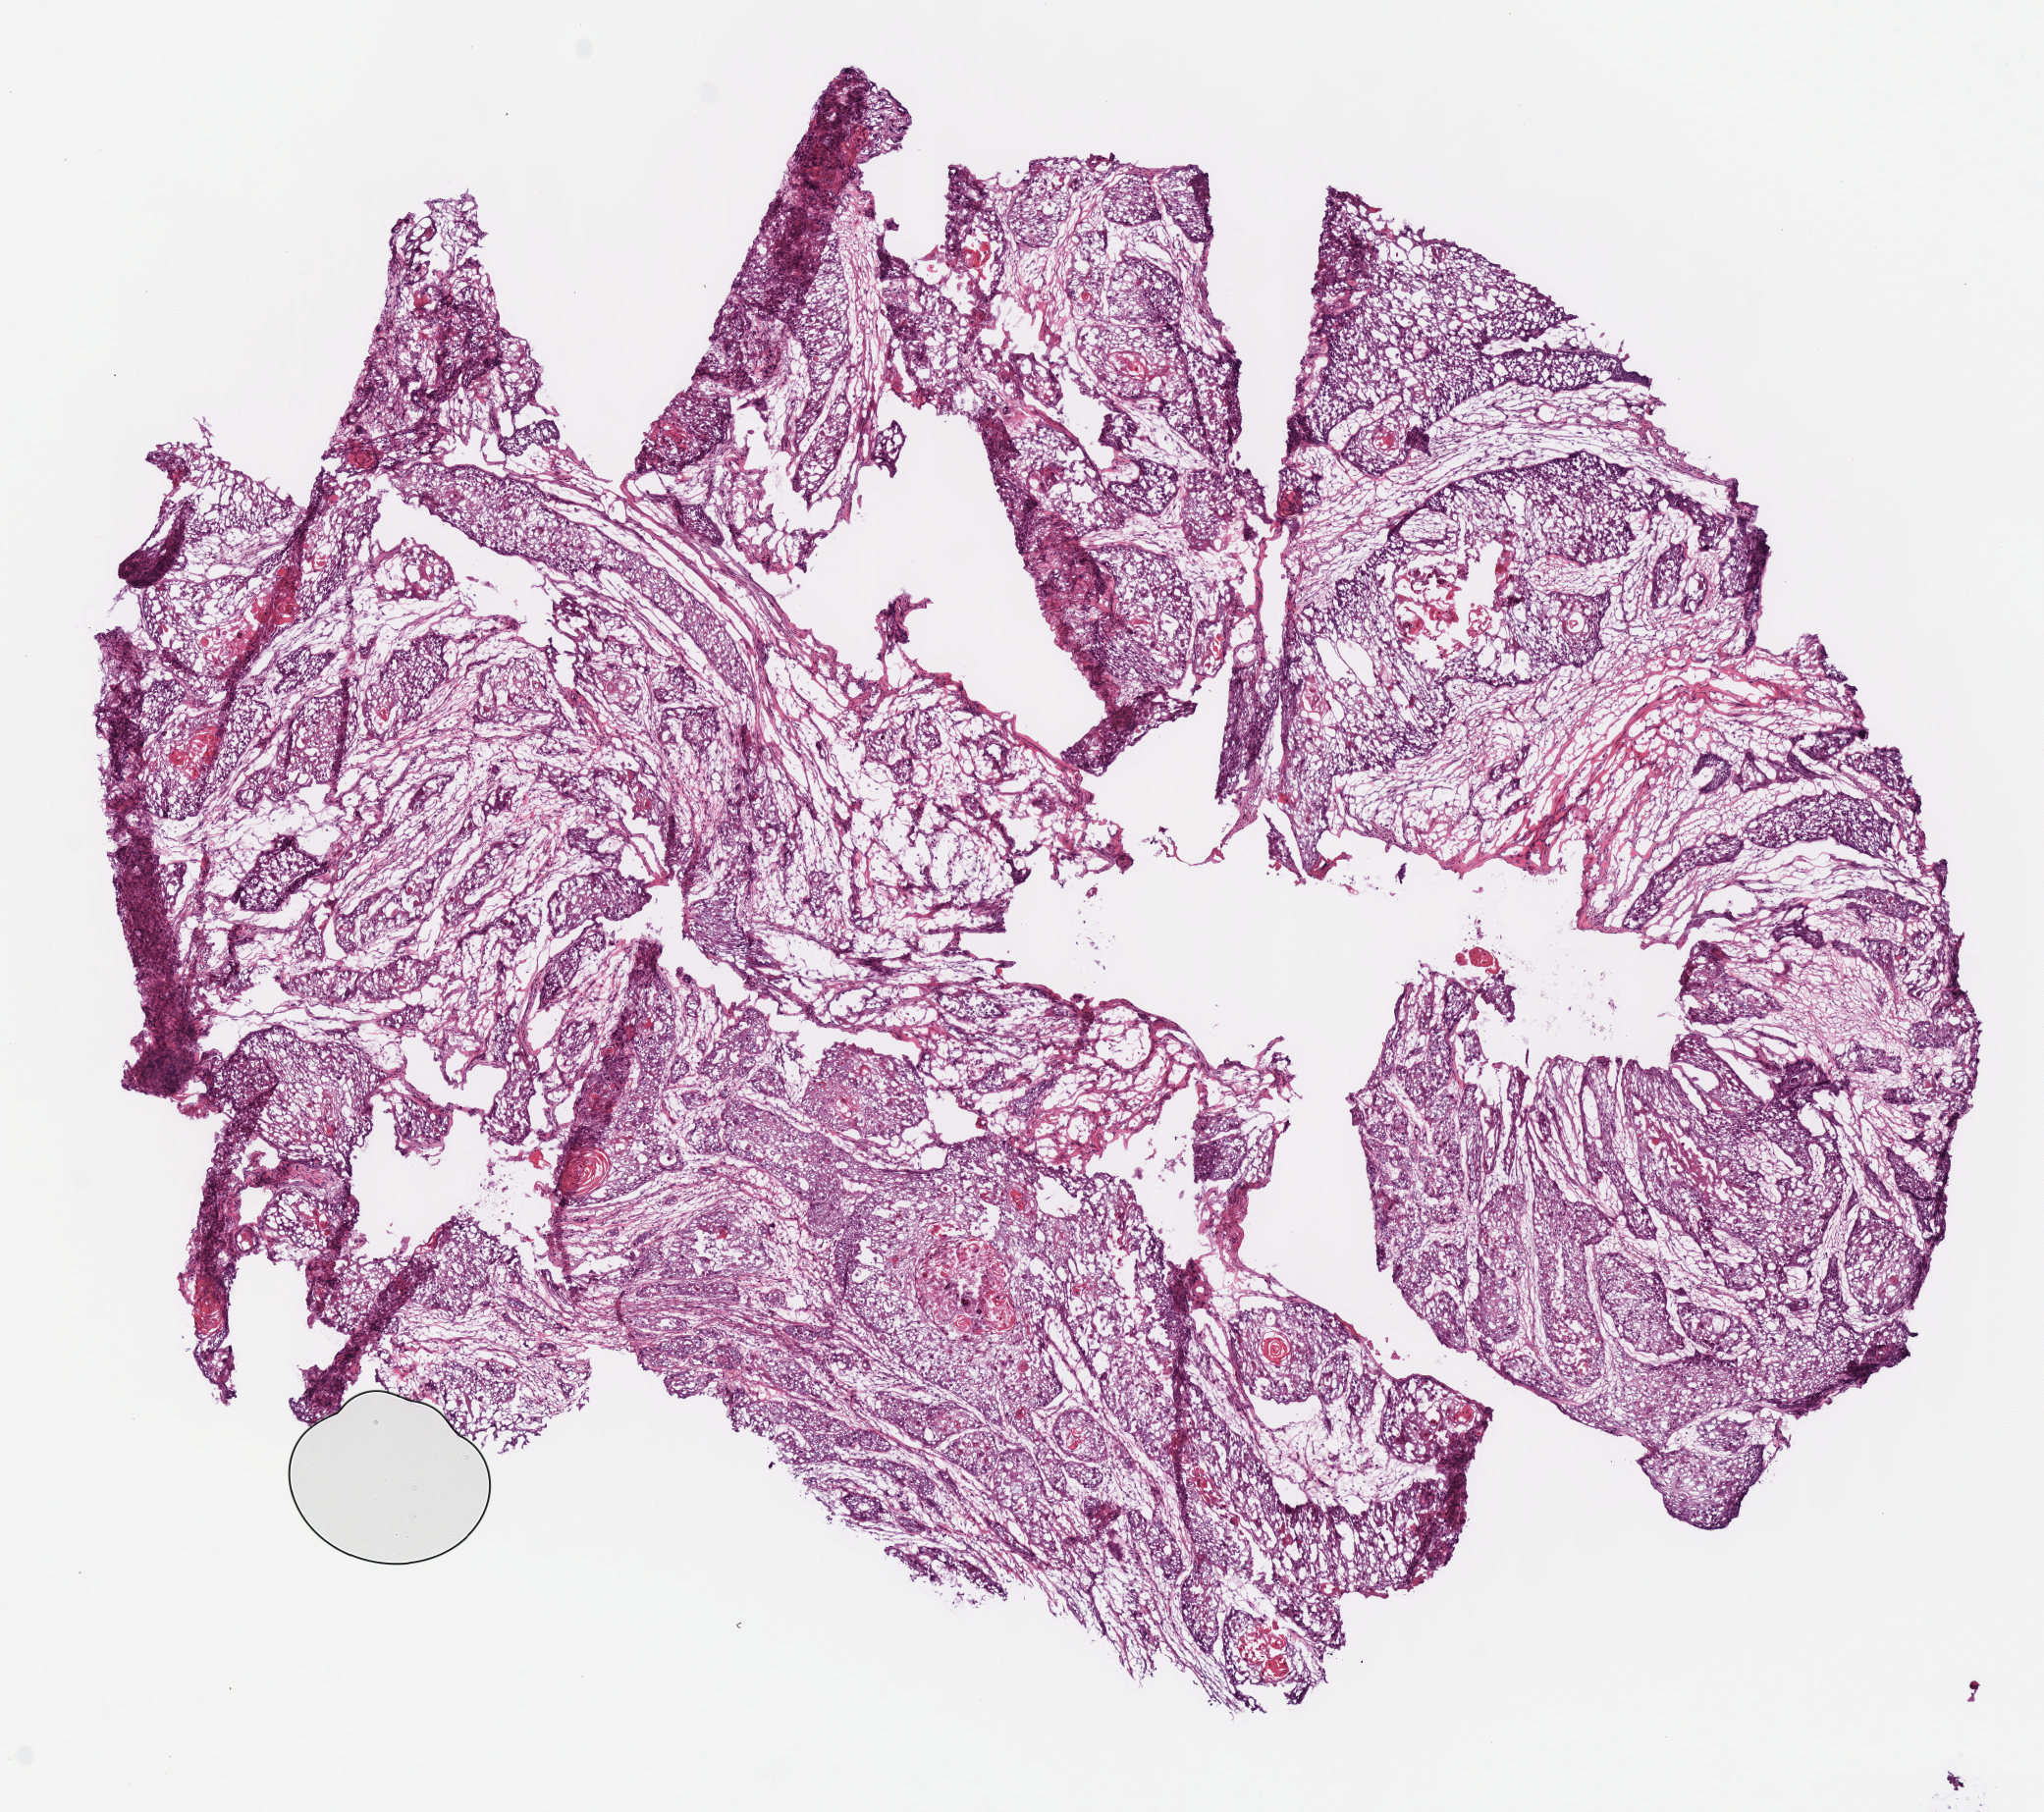
Digitized H&E tissue section (whole slide) — whole scanned area (about 8.2 x 7.3 mm) shown as a low-resolution overview. Frozen section. Sample: primary tumour, head and neck. Female, age 29 years at initial diagnosis. Histologic grade: GX (grade cannot be assessed). Slide review estimates, as recorded: tumour cells 100%, tumour nuclei 75%, normal cells 0%, stromal cells 0%, necrosis 0%. Inflammatory infiltration, as recorded: lymphocyte infiltration 2%, monocyte infiltration 0%, neutrophil infiltration 0%.
Laterality: left. AJCC pathologic stage: IVA (7th edition). Pathologic diagnosis: Squamous cell carcinoma, NOS (overlapping lesion of lip, oral cavity and pharynx).